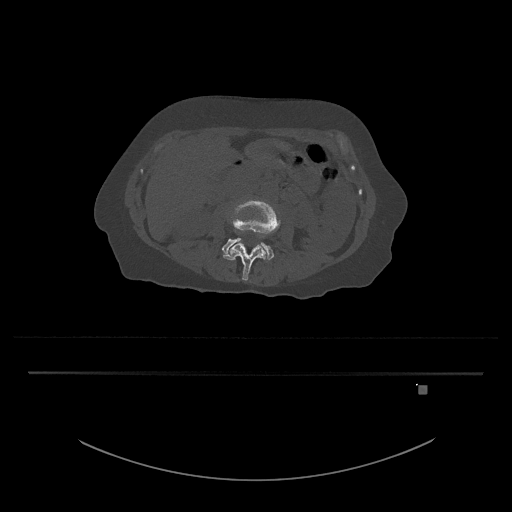
CT including the spine, one axial slice. Position 405 of 797 along the scan axis. Bone window (W 1800 / L 400 HU). 0.5 mm slice thickness. 512 × 512 image matrix, field of view 500 × 500 mm. Patient: female, 57 years. From the clinical record (not read from this slice): primary cancer: cervical.
Outlined on this slice (semi-automatically segmented with operator editing):
- L3 vertebra: bounding box [x1, y1, x2, y2] px = [223, 199, 281, 281]
- L4 vertebra: [222, 238, 274, 262]